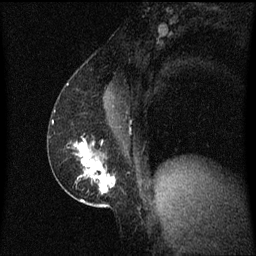
Breast MRI (dynamic contrast-enhanced), one sagittal slice. Position 33 of 60 along the scan axis. Dynamic contrast-enhanced series, image 2 of 3 at this slice position (ordered by acquisition). 1.5 T. TE 4.2 ms, TR 8.4 ms. 2 mm slice thickness. 256 × 256 image matrix. Patient: female, 52 years. Case-level facts recorded for this patient, not image findings: setting: breast cancer imaged before/during neoadjuvant chemotherapy; receptor status: HER2-positive.
Outlined on this slice (semi-automatically segmented with operator editing):
- analysis volume of interest (the breast-tissue region the enhancement analysis was run in; not a lesion): box from (x=62, y=138) to (x=117, y=203) px
- tumour enhancement mask (voxels above the 70 % enhancement threshold inside the analysis volume of interest): (x=75, y=142)–(x=117, y=193)